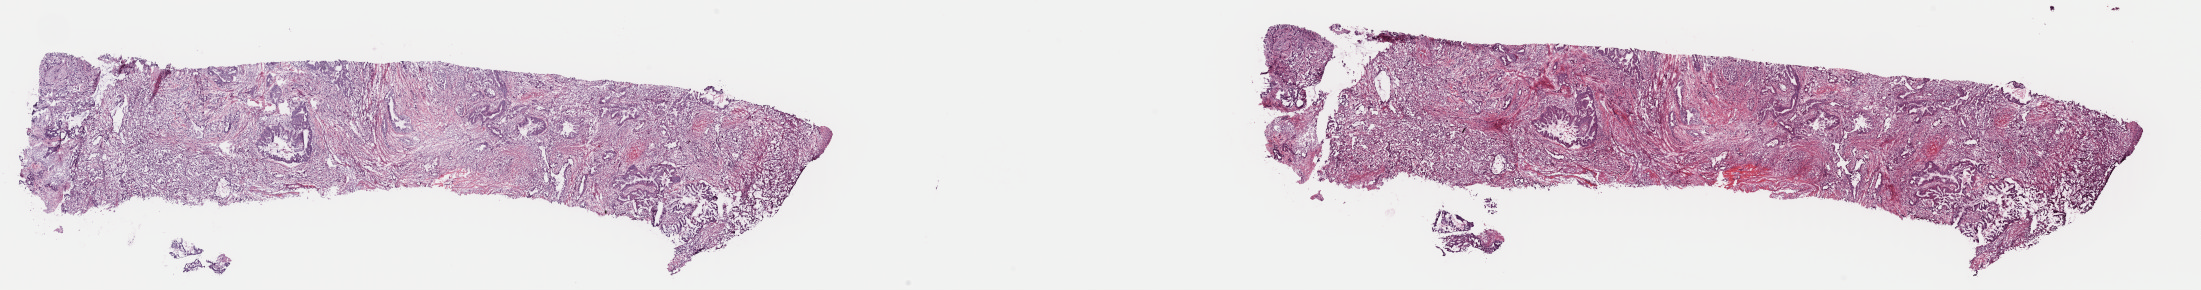
Digitized Hematoxylin and eosin (H&E) stained tissue section (whole slide) — low-resolution overview of the scanned area, about 34.7 x 4.6 mm (from a 40x scan); frozen section from the top of the tissue portion; sample: primary tumour, pancreas. Male, age 75 years at initial diagnosis. Histologic grade: G1 (well differentiated). Slide review estimates, as recorded: tumour cells 100%, tumour nuclei 35%, normal cells 0%, stromal cells 0%, necrosis 0%. Infiltration values recorded for this section: lymphocyte infiltration 10%, monocyte infiltration 0%, neutrophil infiltration 0%.
- AJCC pathologic stage: IIA (7th edition)
- TNM: T3 N0 M0
- lymph nodes positive (case pathology): 0 of 22 examined
- pathologic diagnosis: Infiltrating duct carcinoma, NOS (tail of pancreas)